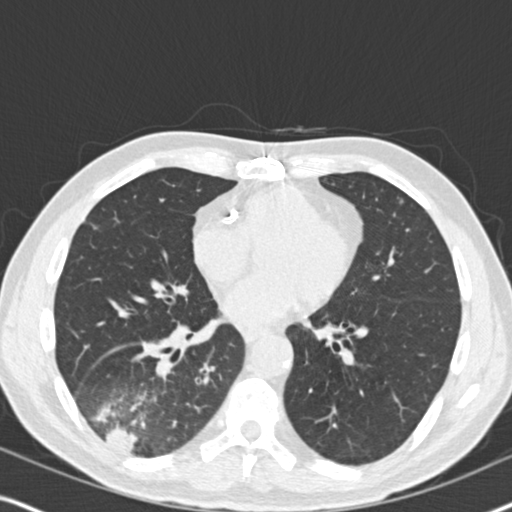
Low-dose screening chest CT, axial slice. Second annual screen. Lung window (W 1500 / L -600 HU). Slice 98 of 182 in the series. 512 × 512 image matrix, field of view 330 × 330 mm. Male, age 61 years at enrolment.
Expert reader's lesion annotation, bounding box <63,346,193,468> (left, top, right, bottom; pixels). The exam's reader record, not a measurement of the box and not confirmed to be the same lesion: non-calcified nodule or mass ≥4 mm, right lower lobe, 90 × 80 mm, soft tissue attenuation, pre-existing on the prior screen: yes; interval growth: yes. Official screen result: positive, other. Later outcome: lung cancer diagnosed 20 days after this screen — bronchiolo-alveolar adenocarcinoma, NOS, right lower lobe, moderately differentiated (G2), stage IIIB (AJCC 6th edition), 90 mm at pathology.